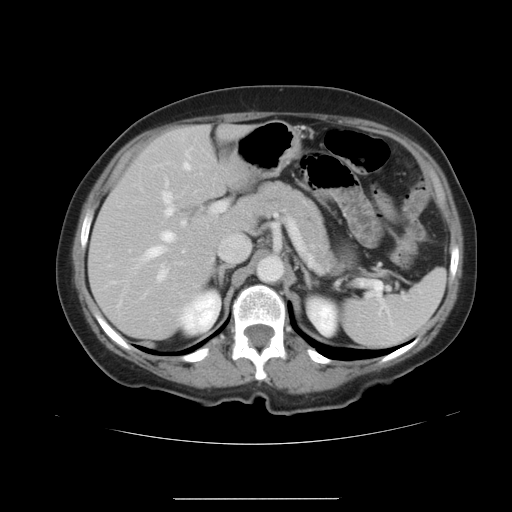
Contrast-enhanced abdominal CT, one axial slice. Slice 24 of 41 in the series (ordered by position). Intravenous contrast given. Soft-tissue window (W 400 / L 40 HU). 5 mm slice thickness. 512 × 512 image matrix. Female patient, age 63 years. Case-level facts recorded for this patient, not image findings: diagnosis: colorectal cancer liver metastases, imaged before liver resection; multiple liver metastases: yes; largest metastasis: 1.5 cm; disease in both lobes: yes.
Outlined on this slice (expert manual segmentation):
- hepatic veins: bounding box [x1, y1, x2, y2] px = [145, 163, 190, 258]
- liver: [90, 125, 257, 339]
- planned liver remnant (the part of the liver to remain after resection): [90, 126, 257, 339]
- portal vein (with intrahepatic branches): [158, 193, 225, 279]